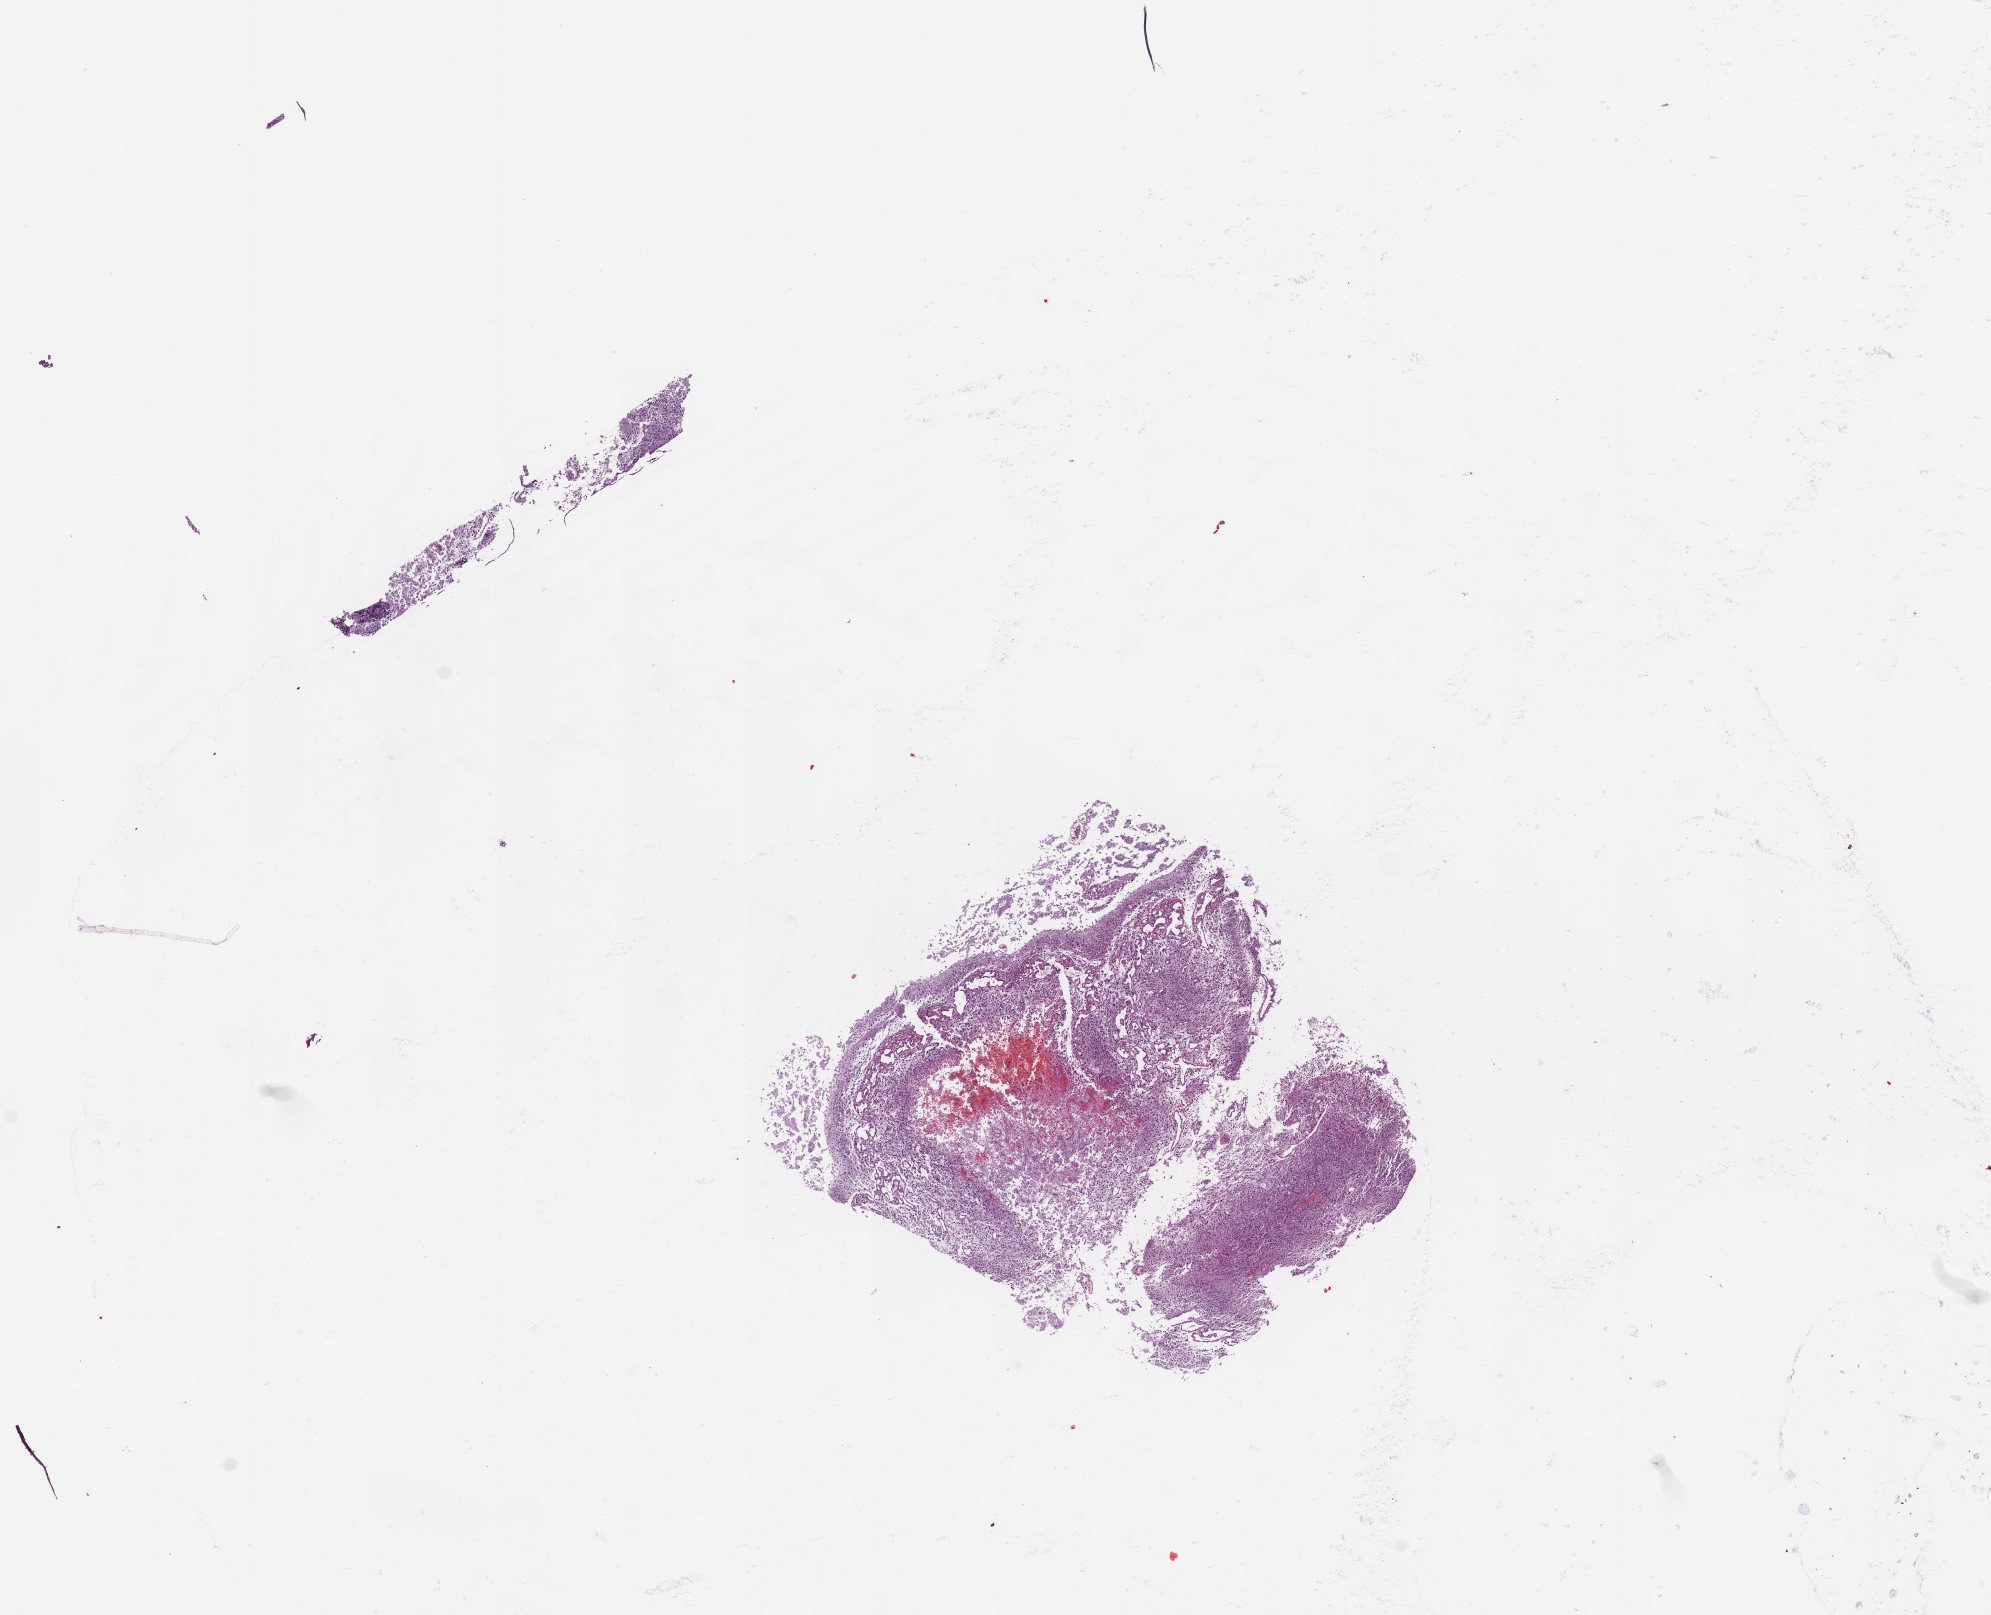
Whole-slide histology image, H&E — whole scanned area (about 15.8 x 12.8 mm, acquisition: 20x scan) shown as a low-resolution overview. Tumour tissue sample, brain. Female, 54 y/o.
Diagnosis: Glioblastoma.